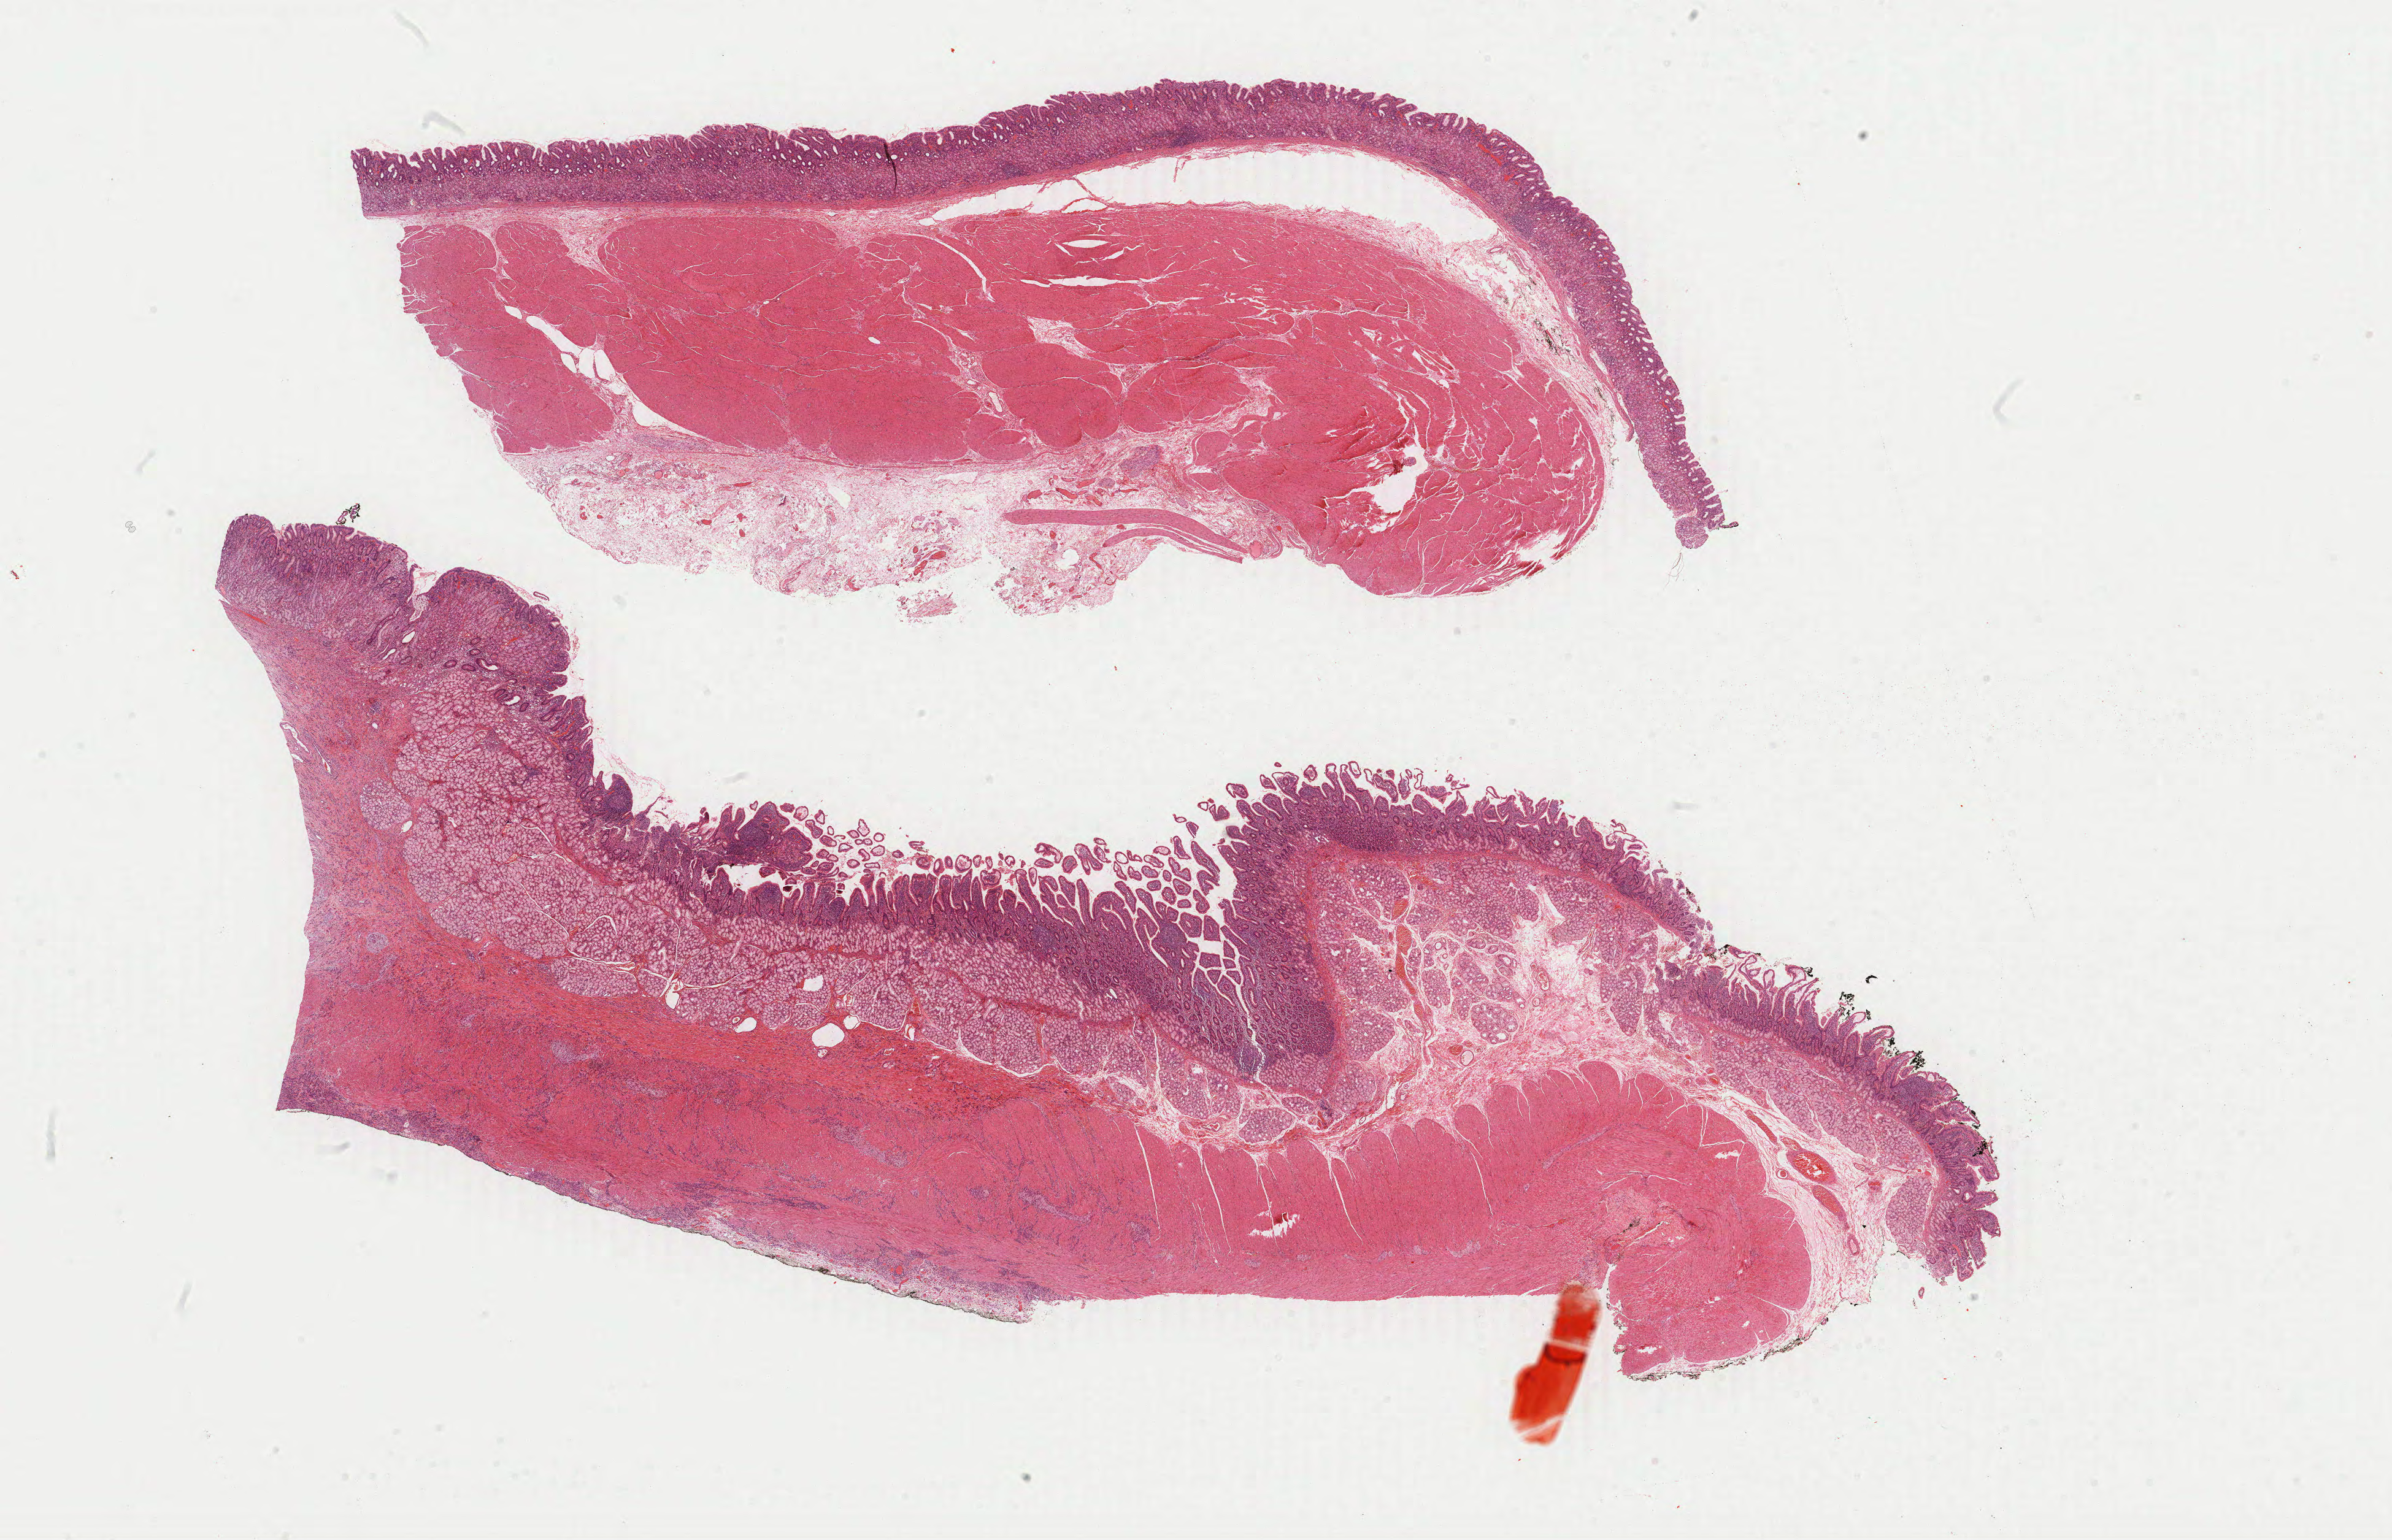
Digitized H&E-stained tissue section (whole slide), a low-resolution overview of the entire scanned area, about 31.3 x 20.2 mm (from a 40x scan). Formalin-fixed paraffin-embedded (FFPE) diagnostic section. Primary tumour sample from the stomach. Female, age 58 years at initial diagnosis. Histologic grade: G3 (poorly differentiated).
Pathologic diagnosis: Carcinoma, diffuse type (gastric antrum). AJCC pathologic stage: IIIA (6th edition). Lymph nodes positive (case pathology): 3 of 7 examined.